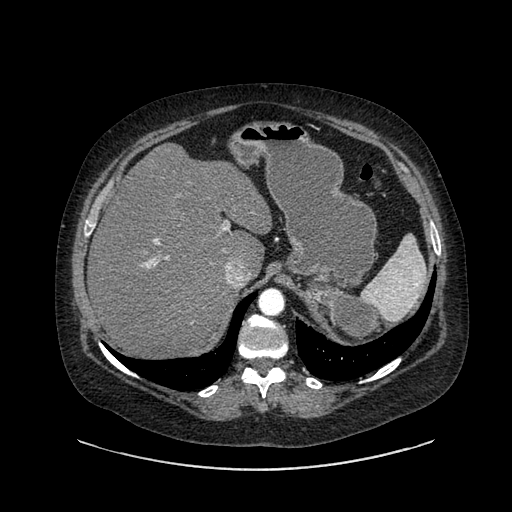
Contrast-enhanced abdominal CT, one axial slice; slice 633 of 769 in the series (ordered by position); reconstruction kernel SOFT; intravenous contrast given; soft-tissue window (W 400 / L 40 HU); 0.62 mm slice thickness; 512 × 512 image matrix. Female patient, age 61 years. Case-level facts recorded for this patient, not image findings: diagnosis: adrenocortical carcinoma; tumour side: left adrenal; tumour size at pathology: 13 cm; Ki-67 index: 79 %; stage (as recorded): 2.
Structures marked on this image (semi-automatic segmentation, software-assisted and operator-edited):
- mass: bounding box [x1, y1, x2, y2] px = [307, 277, 377, 342]